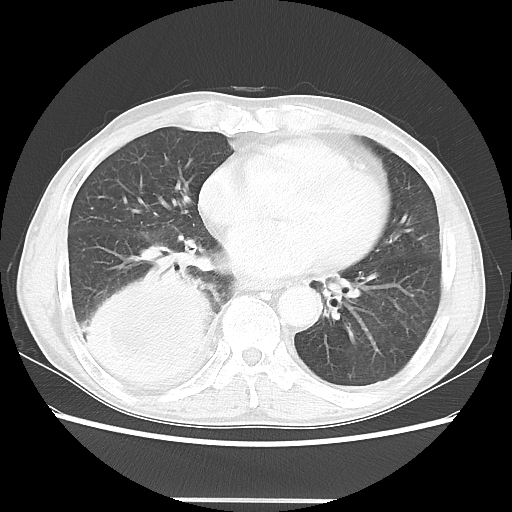
Chest CT, one axial slice. Slice 17 of 48 in the series (ordered by position). Reconstruction kernel LUNG. 100 kVp. Lung window (W 1500 / L -600 HU). 5 mm slice thickness. 512 × 512 image matrix. Male patient, age 66 years. Case-level facts recorded for this patient, not image findings: clinical TNM (as recorded): T4 N1 M1; histopathological grade: G3.
Outlined on this slice (bounding box drawn by a radiologist):
- lung tumour (recorded histology: small cell carcinoma): bounding box (x1, y1, x2, y2) in pixels: (72, 267, 223, 404)